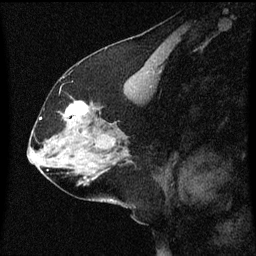
Breast MRI (dynamic contrast-enhanced), one sagittal slice; position 29 of 60 along the scan axis; dynamic contrast-enhanced series, image 2 of 3 at this slice position (ordered by acquisition); 1.5 T; TE 4.2 ms, TR 8 ms; 256 × 256 image matrix. Female patient, age 58 years.
Annotated regions visible in this slice (semi-automatically segmented with operator editing):
- analysis volume of interest (the breast-tissue region the enhancement analysis was run in; not a lesion): bounding box (x1, y1, x2, y2) in pixels: (56, 102, 95, 137)
- tumour enhancement mask (voxels above the 70 % enhancement threshold inside the analysis volume of interest): (66, 102, 89, 121)